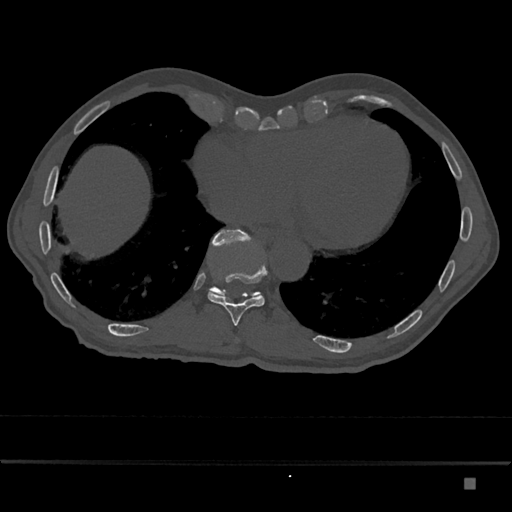
CT including the spine, one axial slice; slice 728 of 797 in the series (ordered by position); 120 kVp; bone window (W 1800 / L 400 HU); 0.5 mm slice thickness; 512 × 512 image matrix. Male patient, age 72 years. Case-level facts recorded for this patient, not image findings: primary cancer: prostate.
Outlined on this slice (semi-automatically segmented with operator editing):
- T10 vertebra: box from (x=208, y=267) to (x=267, y=326) px
- T11 vertebra: (x=209, y=229)–(x=261, y=300)